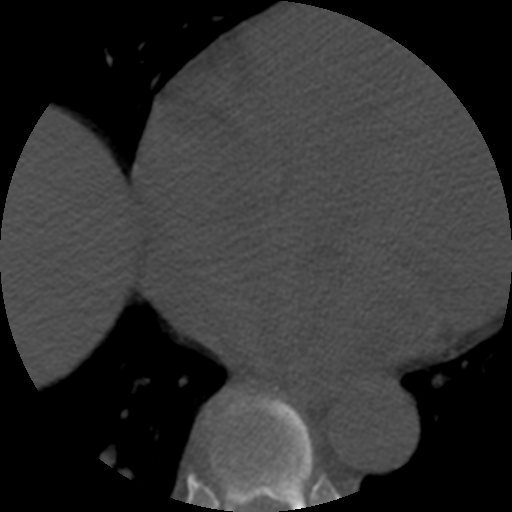
CT including the spine, one axial slice; slice 320 of 508 in the series (ordered by position); reconstruction kernel STANDARD; 120 kVp; bone window (W 1800 / L 400 HU); 1.25 mm slice thickness; 512 × 512 image matrix, field of view 160 × 160 mm. Patient age 57 years. From the clinical record (not read from this slice): primary cancer: prostate.
Outlined on this slice (semi-automatically segmented with operator editing):
- T8 vertebra: bounding box (x1, y1, x2, y2) in pixels: (210, 392, 315, 512)